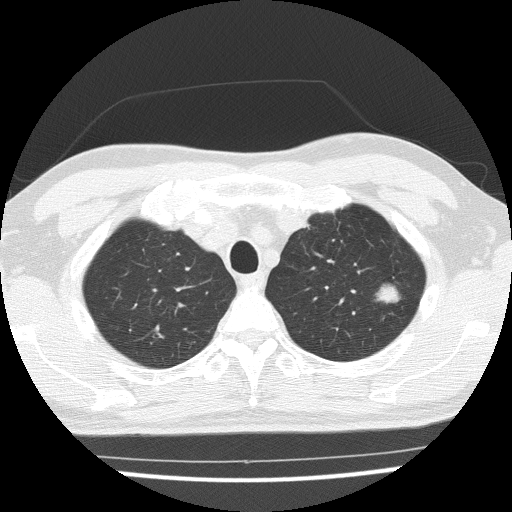
Low-dose screening chest CT, one axial slice. Position 123 of 154 along the scan axis. Reconstruction kernel FC51. Lung window (W 1500 / L -600 HU). 2 mm slice thickness. 512 × 512 image matrix, field of view 330 × 330 mm.
Annotated regions visible in this slice (outlined manually by an expert reader):
- lesion 1 (tumor, upper lobe of left lung): bounding box (x1, y1, x2, y2) in pixels: (377, 285, 399, 303)